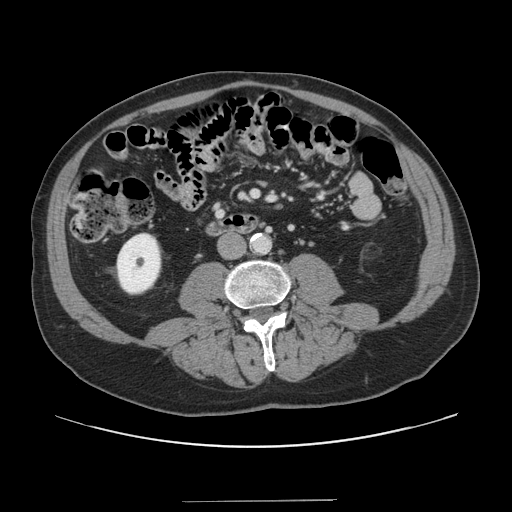
Contrast-enhanced abdominal CT, one axial slice; position 22 of 151 along the scan axis; intravenous contrast given; soft-tissue window (W 400 / L 40 HU); 2.5 mm slice thickness; 512 × 512 image matrix. Male patient, age 63 years. From the clinical record (not read from this slice): diagnosis: colorectal cancer liver metastases, imaged before liver resection; multiple liver metastases: no; largest metastasis: 2.1 cm.
Annotated regions visible in this slice (expert manual segmentation):
- portal vein (with intrahepatic branches): box from (x=253, y=192) to (x=257, y=196) px